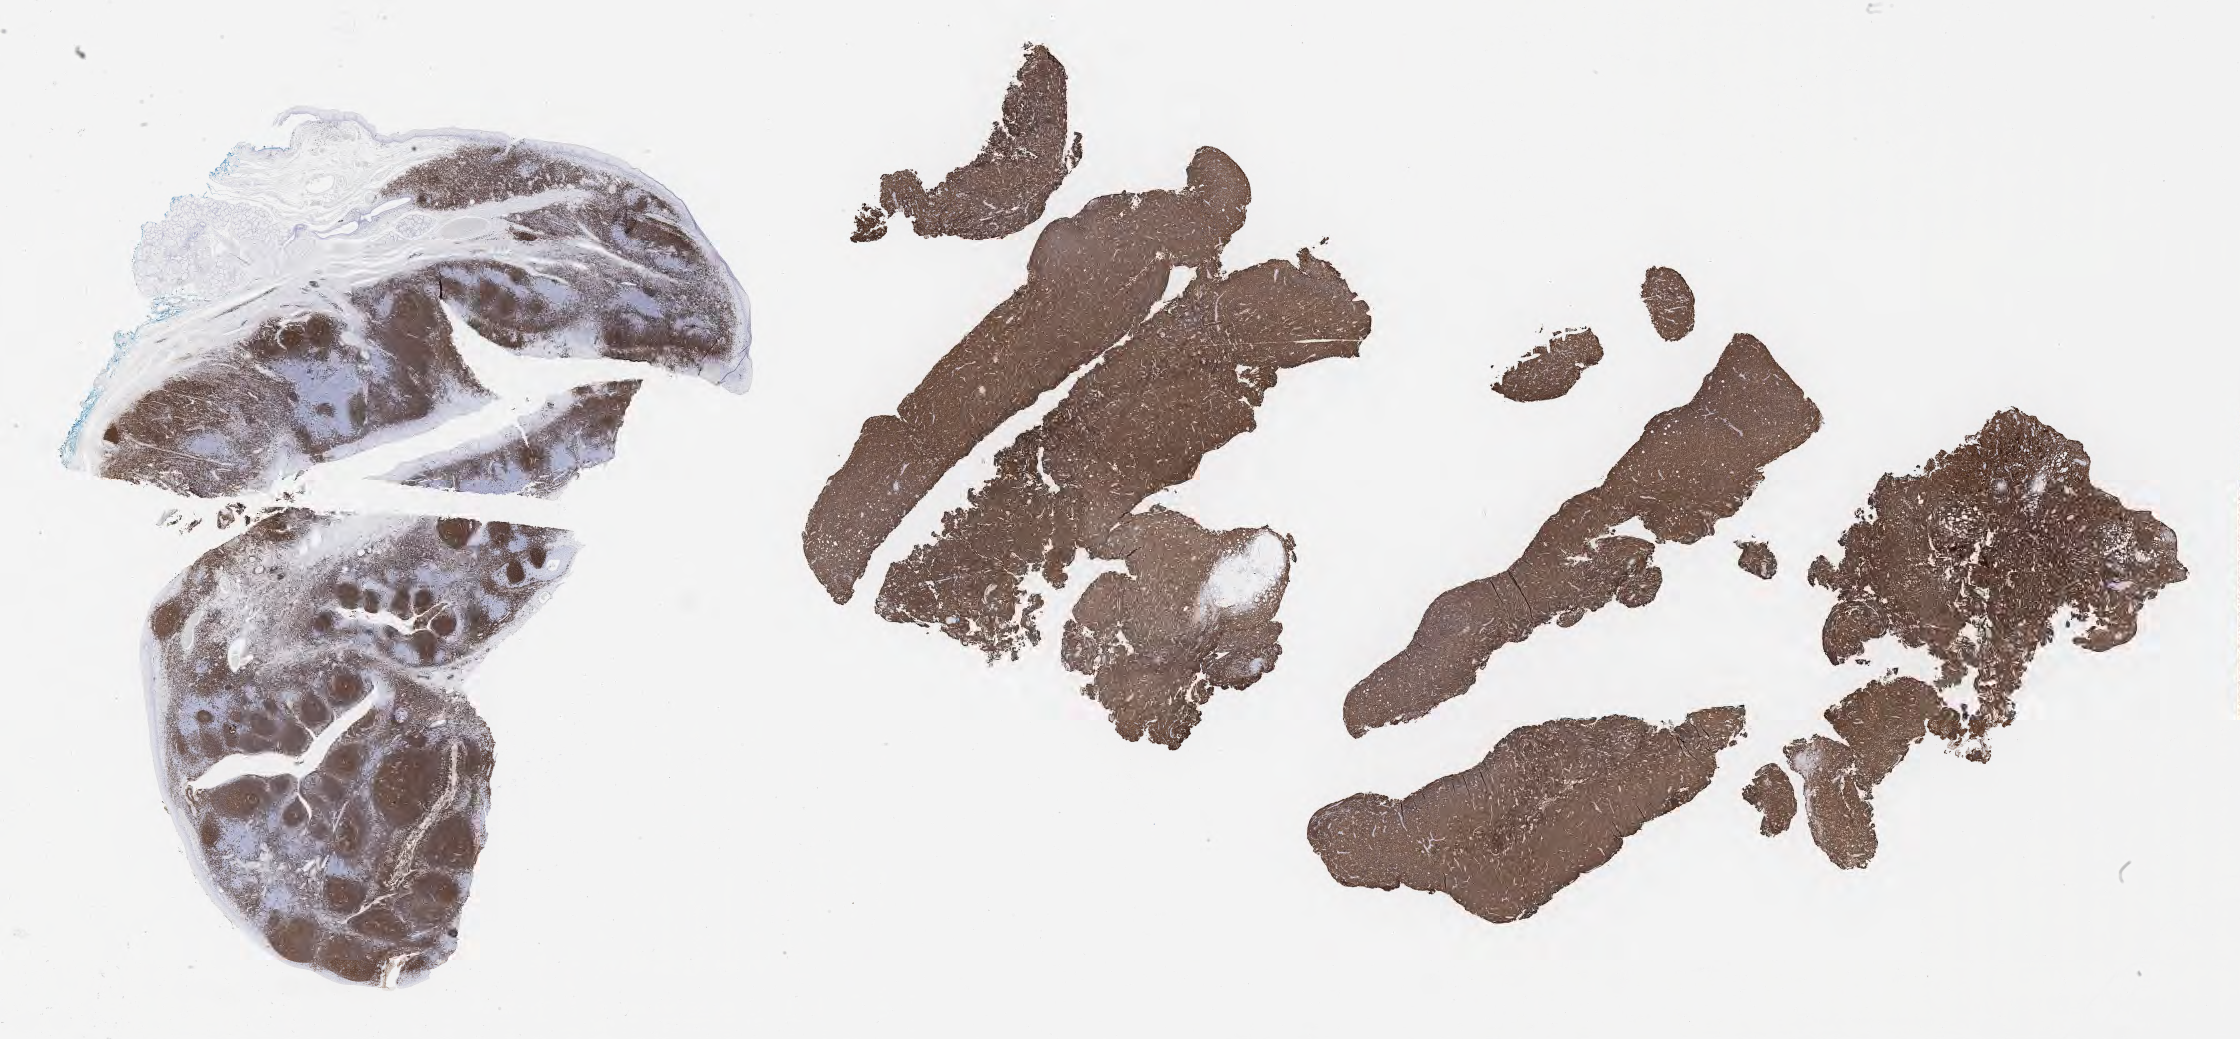
IHC for CD20, whole-slide image, whole scanned area (about 36.2 x 16.8 mm) shown as a low-resolution overview. Tumor tissue. Patient male; 45 years old.
* histologic diagnosis: Diffuse large B-cell lymphoma, NOS